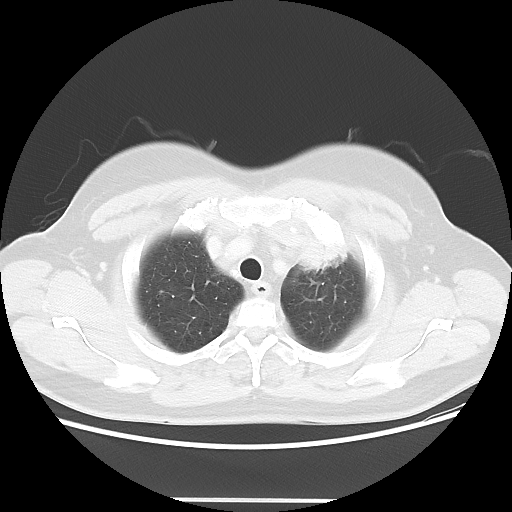
Chest CT, one axial slice. Slice 46 of 52 in the series (ordered by position). Reconstruction kernel LUNG. 120 kVp. Lung window (W 1500 / L -600 HU). 5 mm slice thickness. 512 × 512 image matrix. Patient: female, 52 years. From the clinical record (not read from this slice): clinical TNM (as recorded): T2 N3 M0.
Structures marked on this image (bounding box drawn by a radiologist):
- lung tumour (recorded histology: adenocarcinoma): bounding box [x1, y1, x2, y2] px = [294, 221, 357, 275]